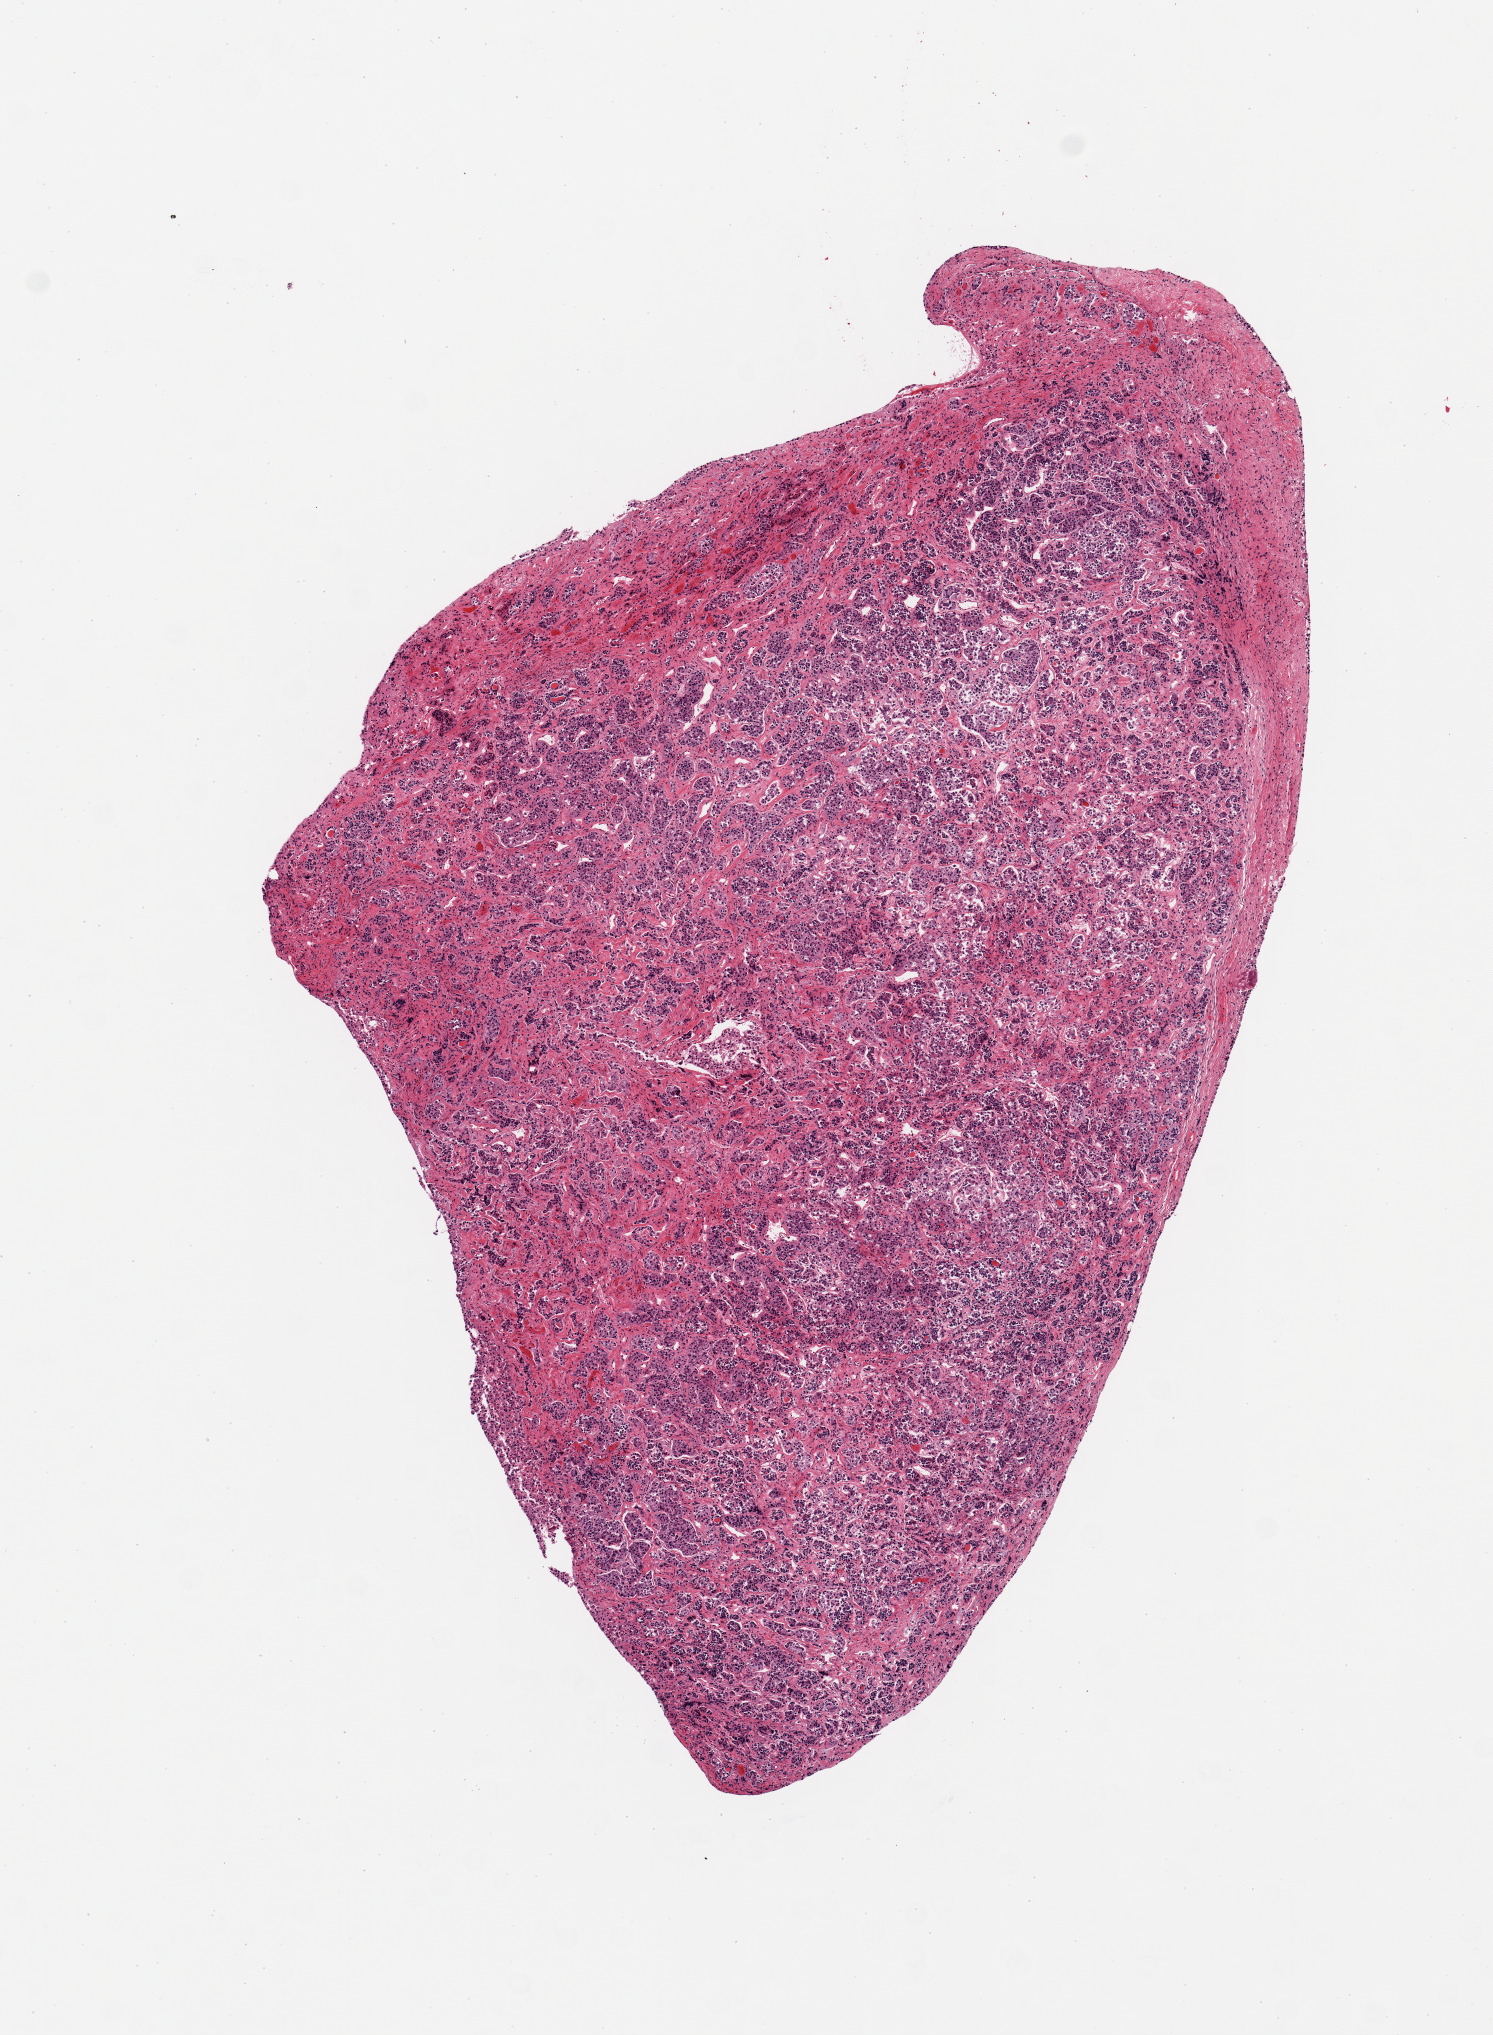
Whole-slide image, hematoxylin and eosin (H&E) stain — shown as a low-resolution overview of the whole scanned area (about 5.9 x 8.1 mm, acquisition: 20x scan), PAXgene-fixed, paraffin-embedded tissue, section of pituitary (target tissue), donor tissue sample. Donor sex: male.
- review note (as recorded): 1 piece; adenohypophysis